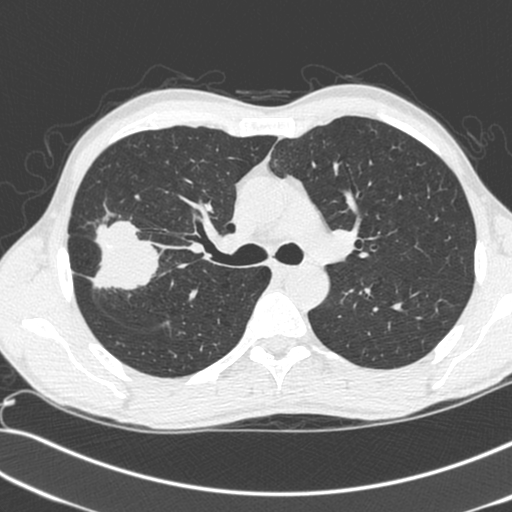
Chest CT (low-dose screening protocol), one axial image, baseline annual screen, lung window (W 1500 / L -600 HU), standard (soft-tissue) reconstruction kernel (C), 512 × 512 image matrix, field of view 341 × 341 mm. Male participant, aged 55 years at enrolment. Current smoker at enrolment.
- Lesion marked by an expert reader, bounding box (x1, y1, x2, y2) in pixels: (68, 223, 156, 299).
- Reader record for this screening exam (exam-level; its link to the box is not recorded): non-calcified nodule or mass ≥4 mm, right upper lobe, 52 × 39 mm, spiculated (stellate) margins, soft tissue attenuation.